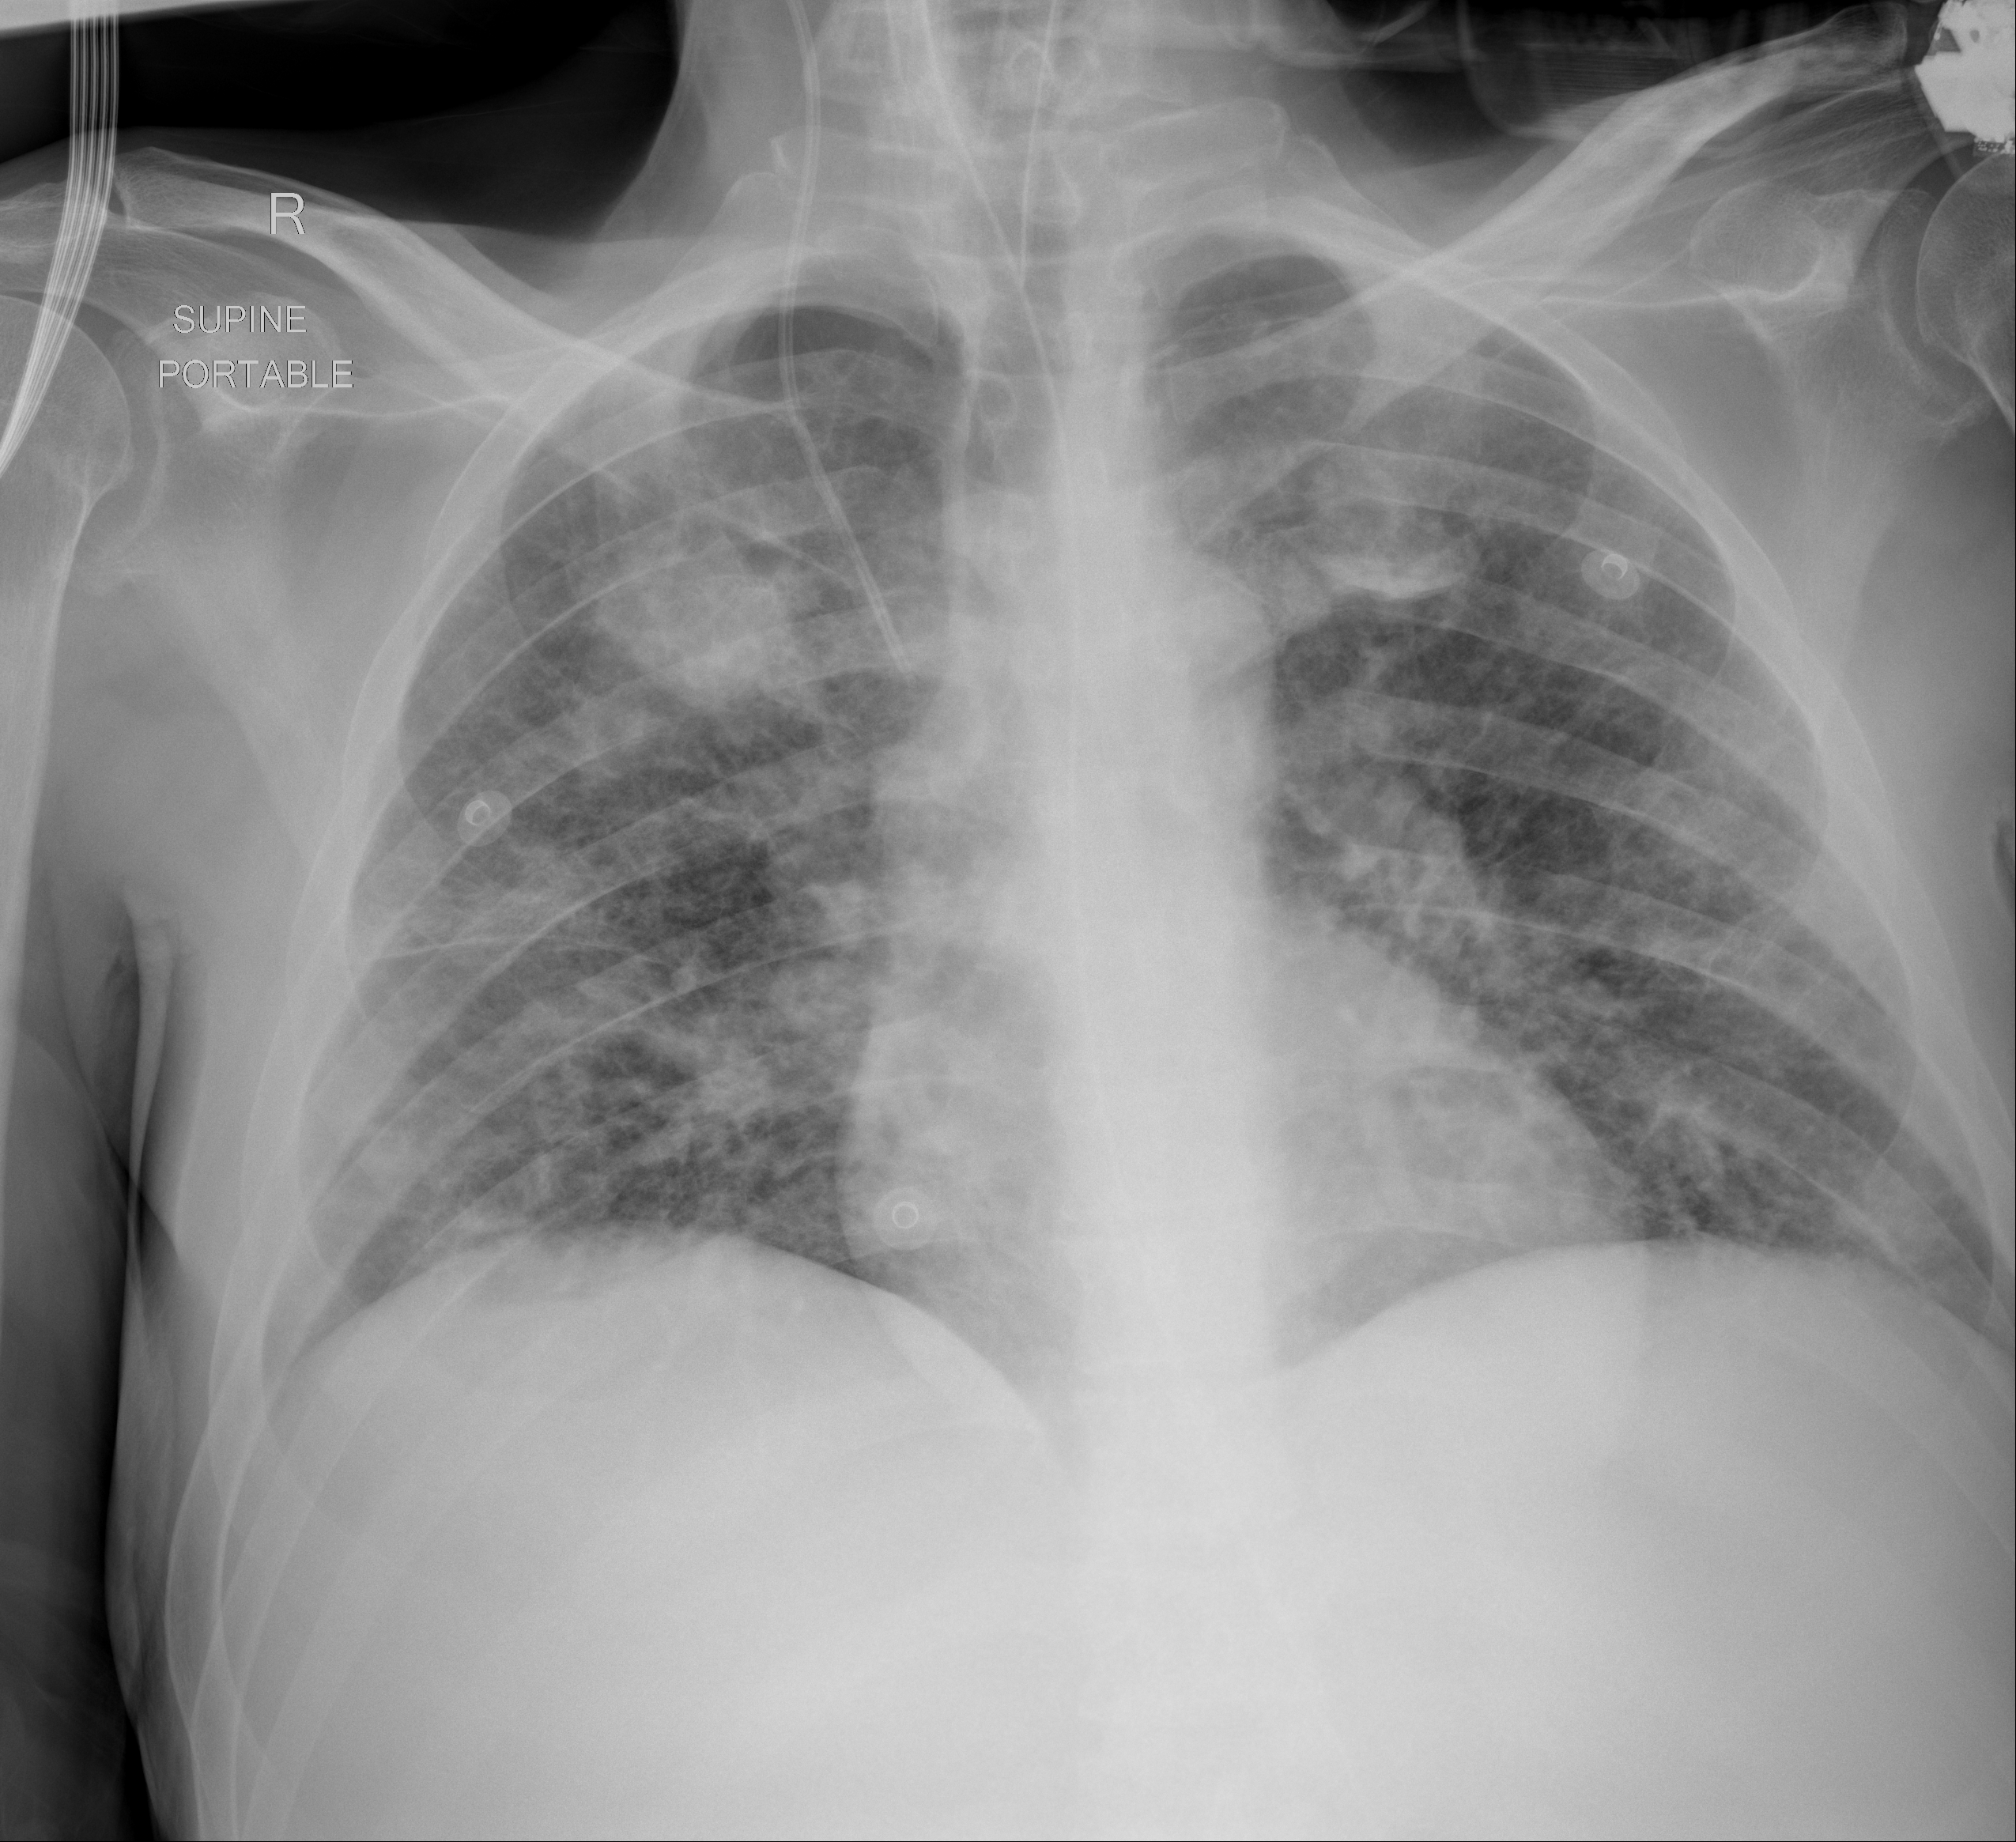
Chest X-ray (portable), AP projection. Male patient, age 54 years; imaged 7 days after the COVID-19 diagnosis.
Radiologist key findings (as recorded): Interval improved aeration from previous exam. Patchy opacities throughout the right upper, mid, and bilateral lower lungs.